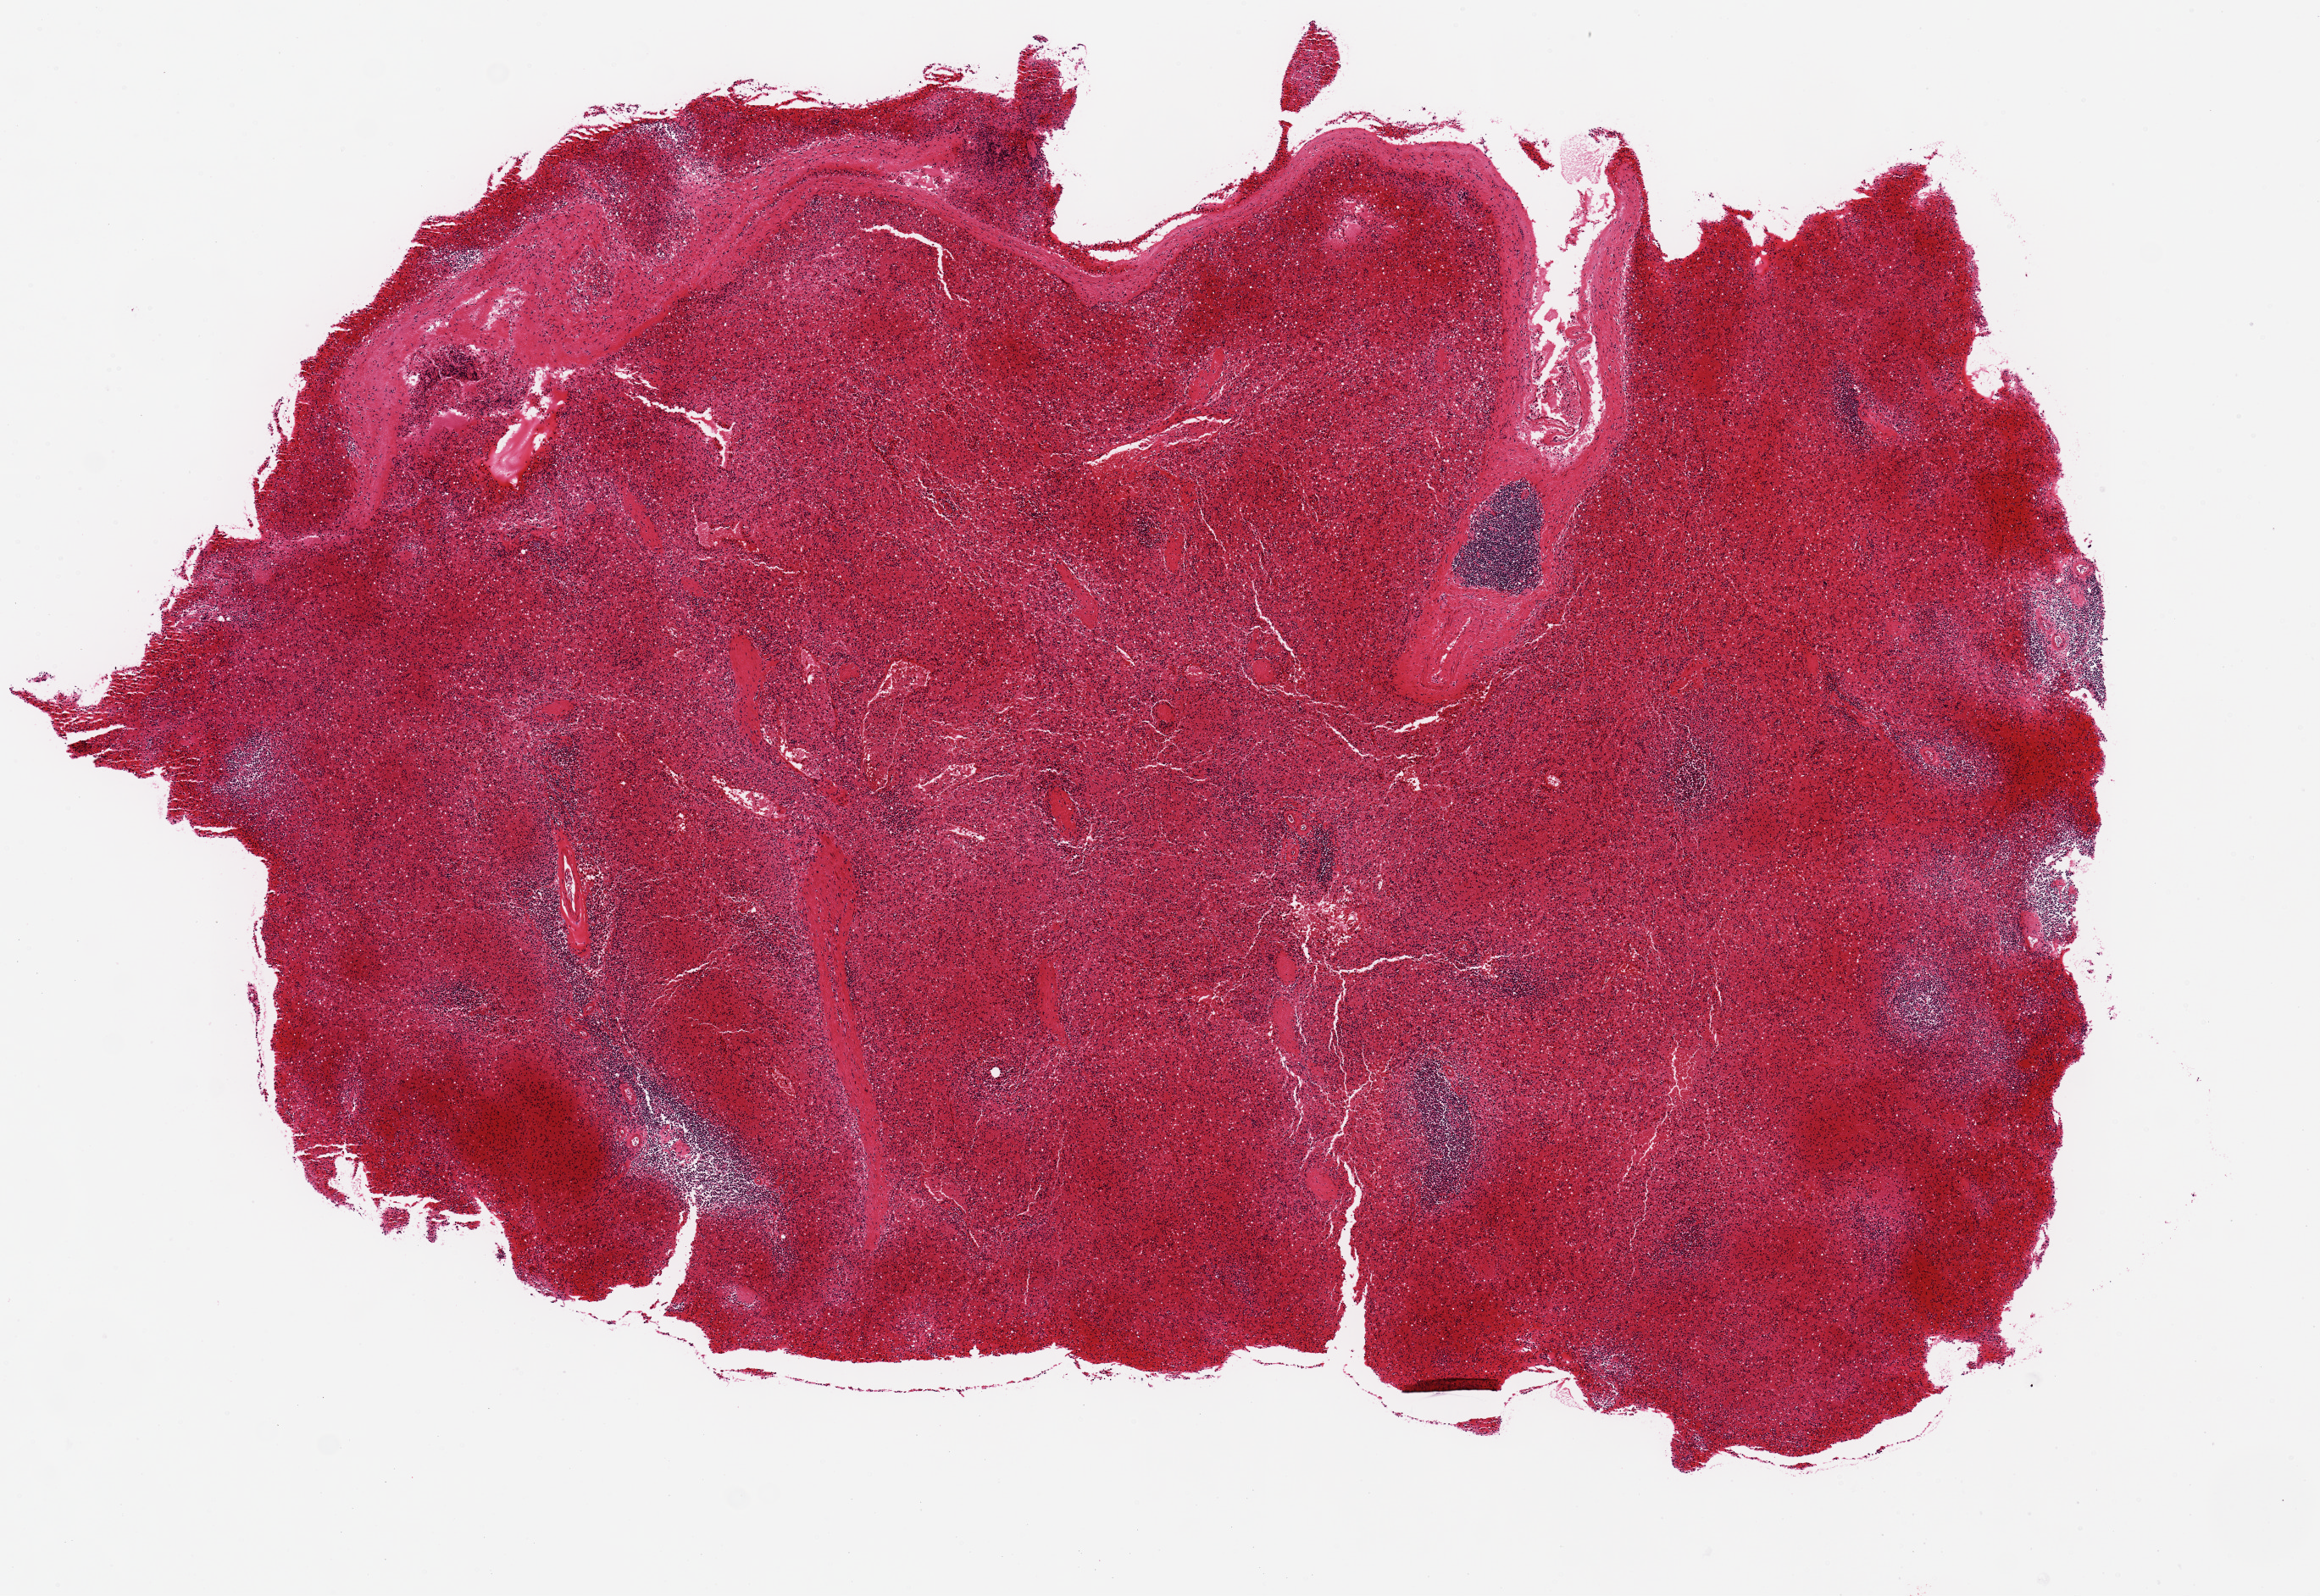
Digitized haematoxylin and eosin-stained section — whole scanned area (about 10.8 x 7.5 mm) shown as a low-resolution overview. PAXgene-fixed, paraffin-embedded tissue. Sampled site (target tissue): spleen. Tissue donor sample. Female donor.
* reviewer comment on this tissue sample: Moderate congestion